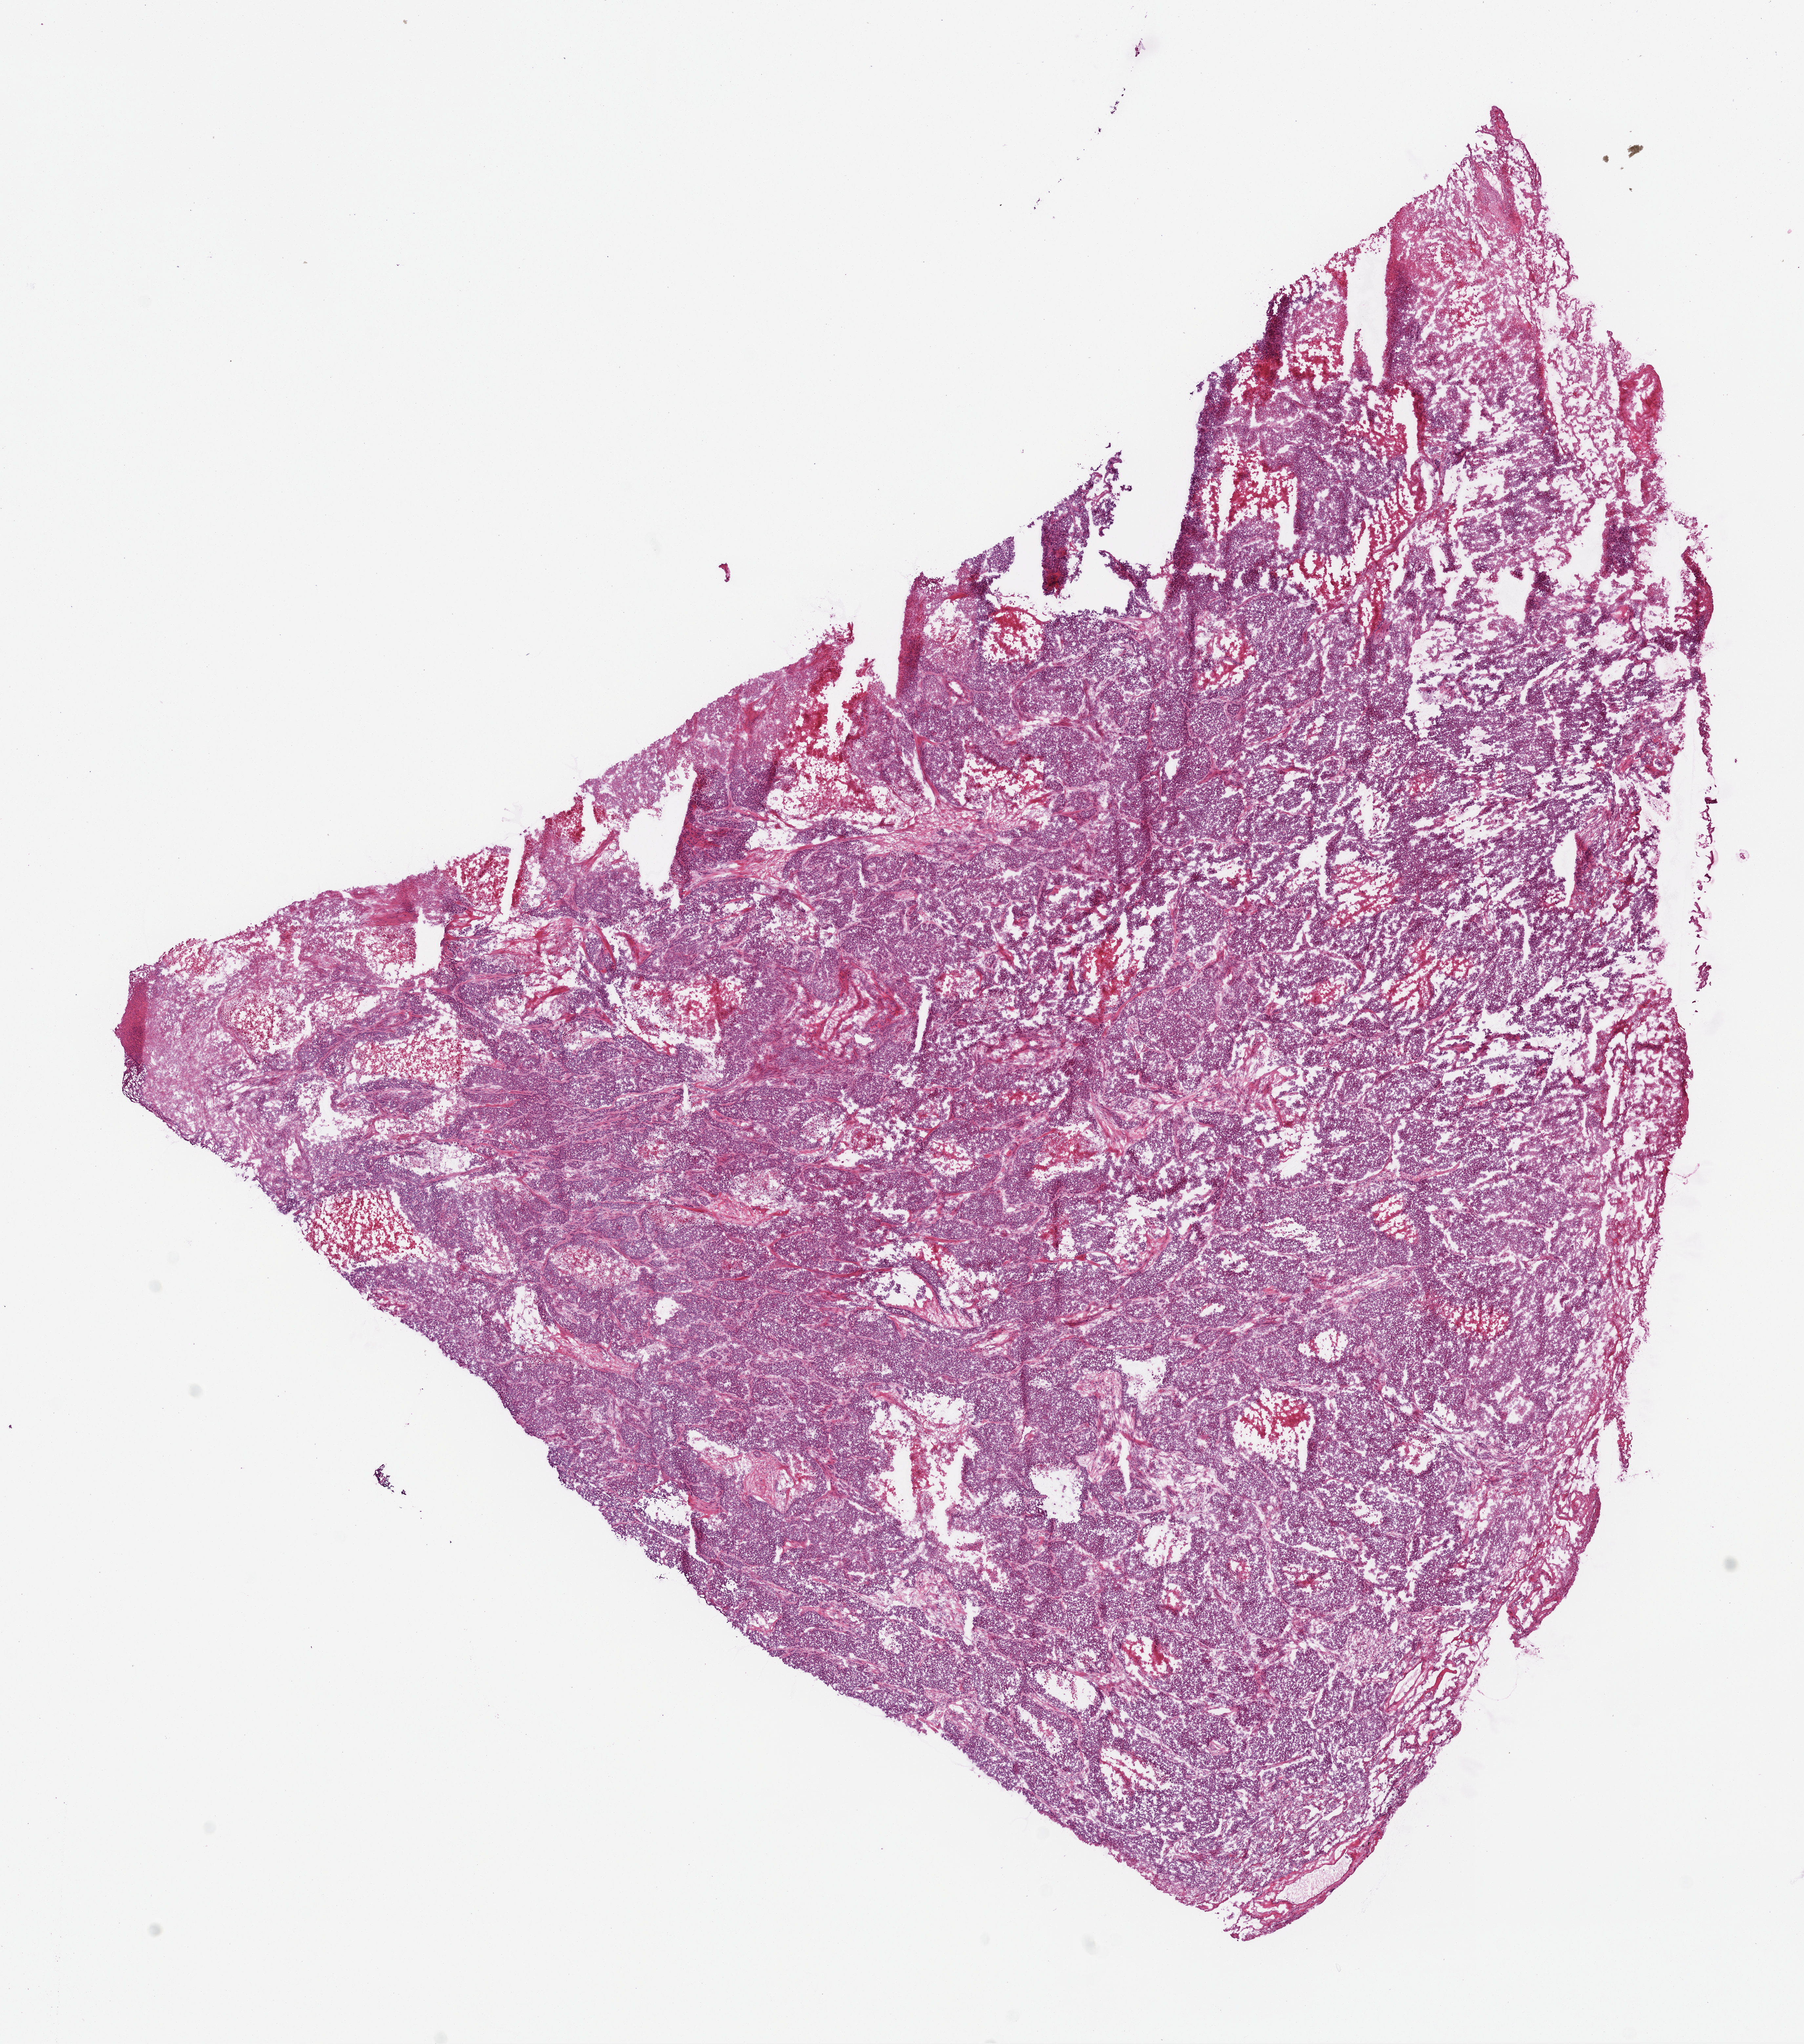
Digitized H&E tissue section (whole slide) — shown as a low-resolution overview of the whole scanned area (about 11.0 x 12.5 mm). Frozen section from the bottom of the tissue portion. Sample: primary tumour, lung. Male patient; age at initial diagnosis 68 years. Pathologist review of this section (percent, as recorded): tumour cells 75%, tumour nuclei 85%, normal cells 0%, stromal cells 5%, necrosis 20%.
Laterality: right. Diagnosis: Squamous cell carcinoma, NOS. AJCC pathologic stage: IB (7th edition).